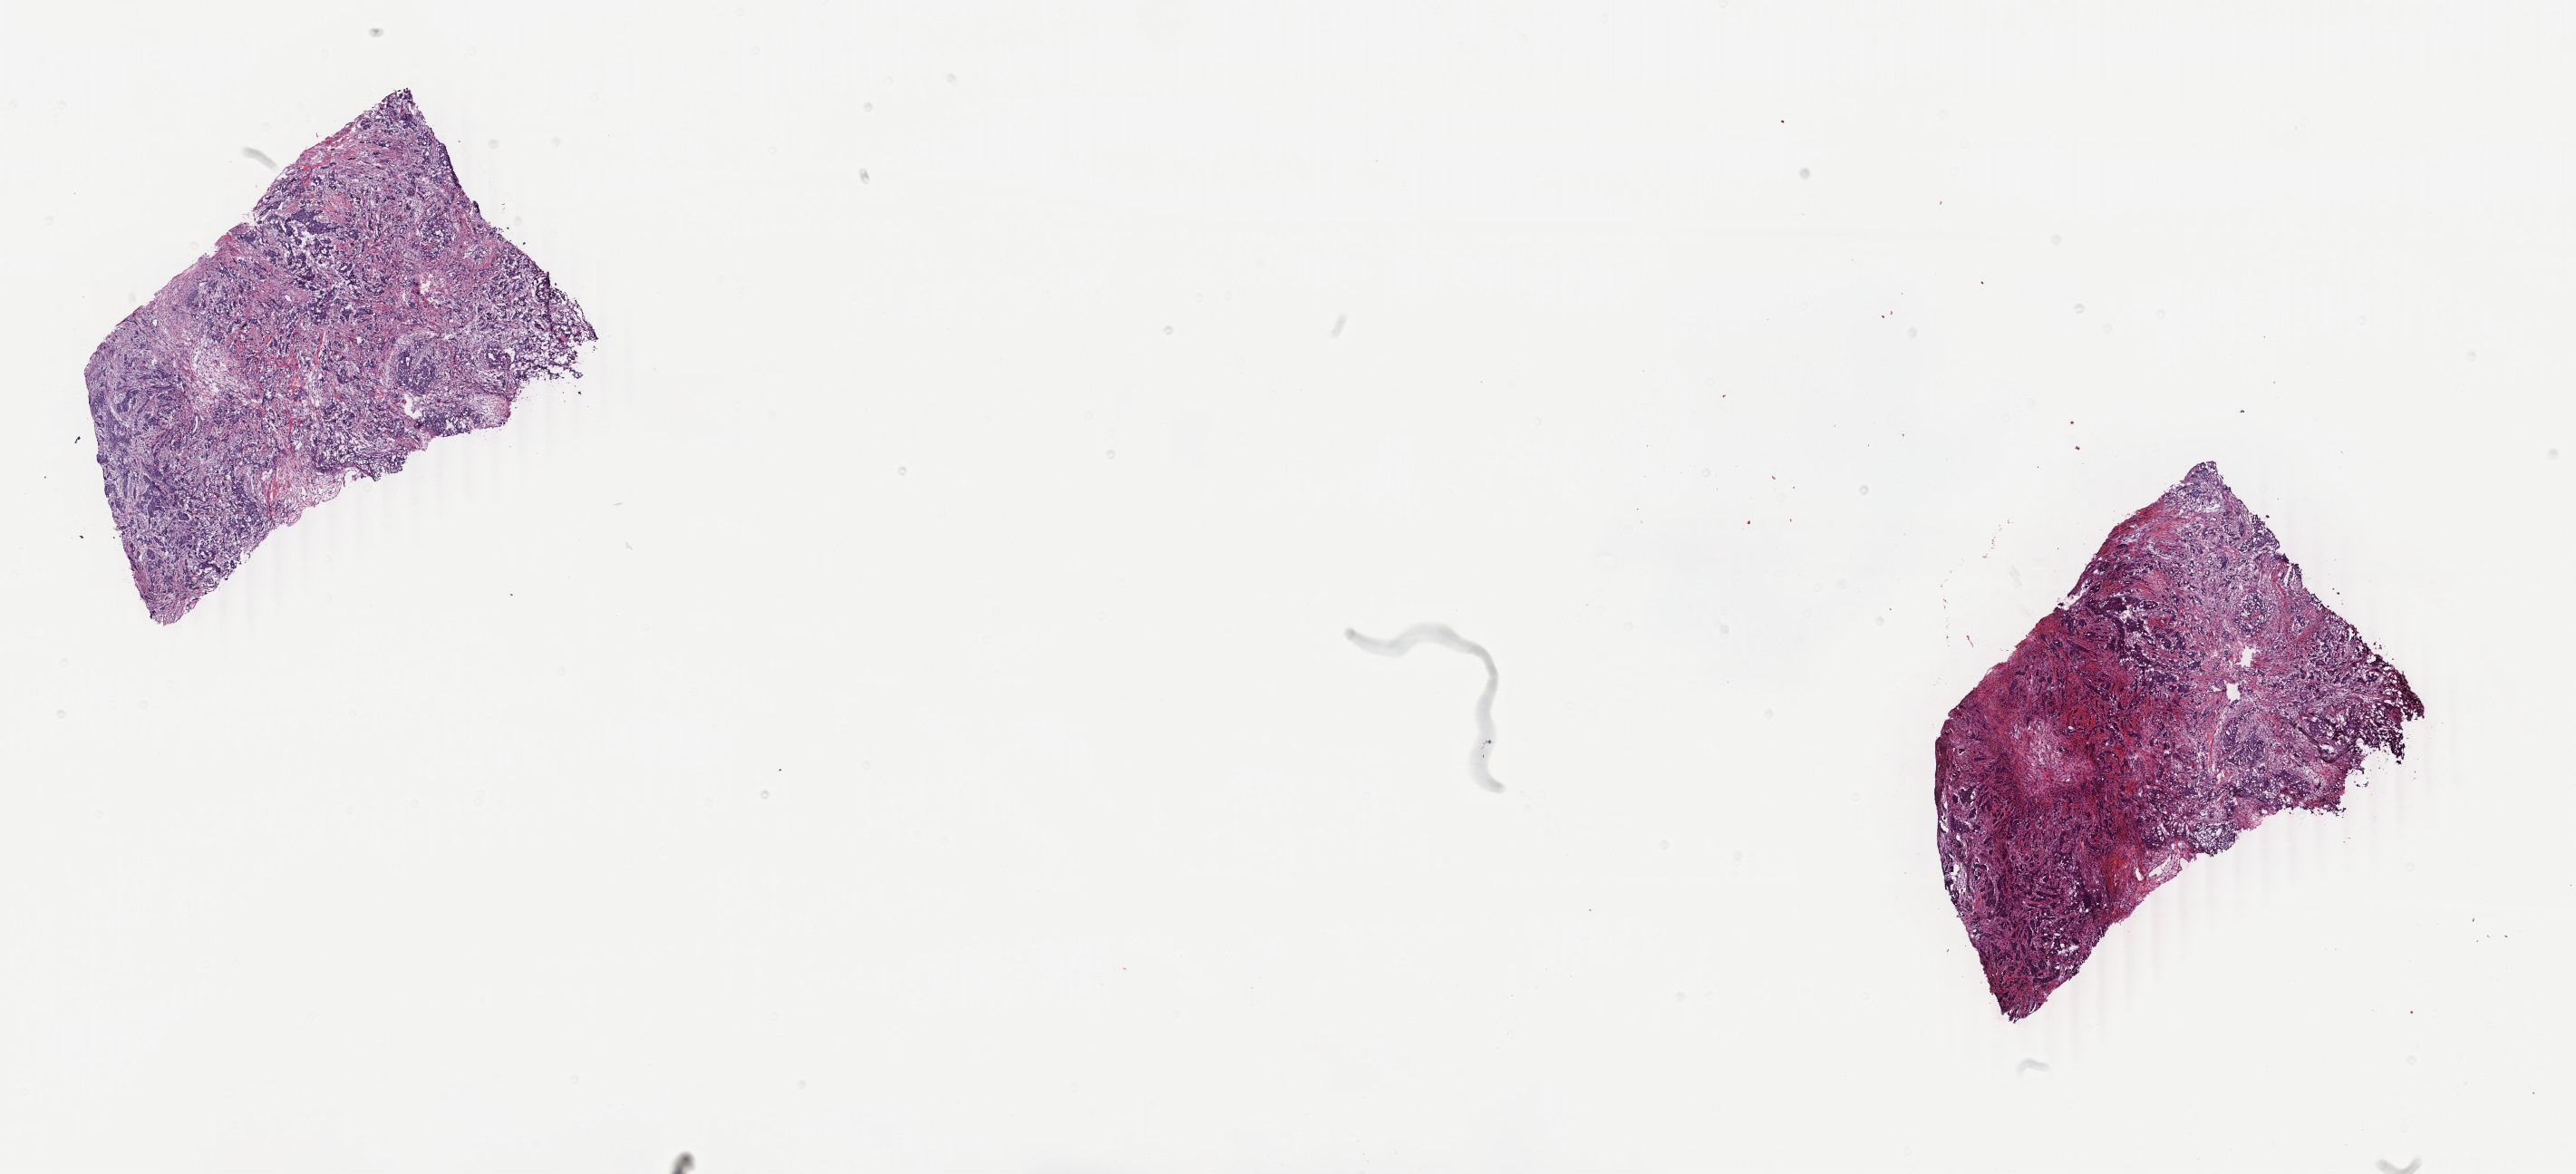
H&E whole-slide image, low-resolution overview of the scanned area, about 22.6 x 10.3 mm (slide scanned at 40x), frozen section, sample: primary tumour, breast. Female, age 44 years at initial diagnosis. Slide review estimates, as recorded: tumour cells 70%, tumour nuclei 60%, normal cells 0%, stromal cells 30%, necrosis 0%. Inflammatory infiltration, as recorded: lymphocyte infiltration 0%, monocyte infiltration 0%, neutrophil infiltration 0%.
AJCC pathologic stage: IIIB (3rd edition). Lymph nodes positive (case pathology): 6 of 15 examined. Laterality: right. TNM: T4b N1b M0. Histologic diagnosis: Infiltrating duct carcinoma, NOS.